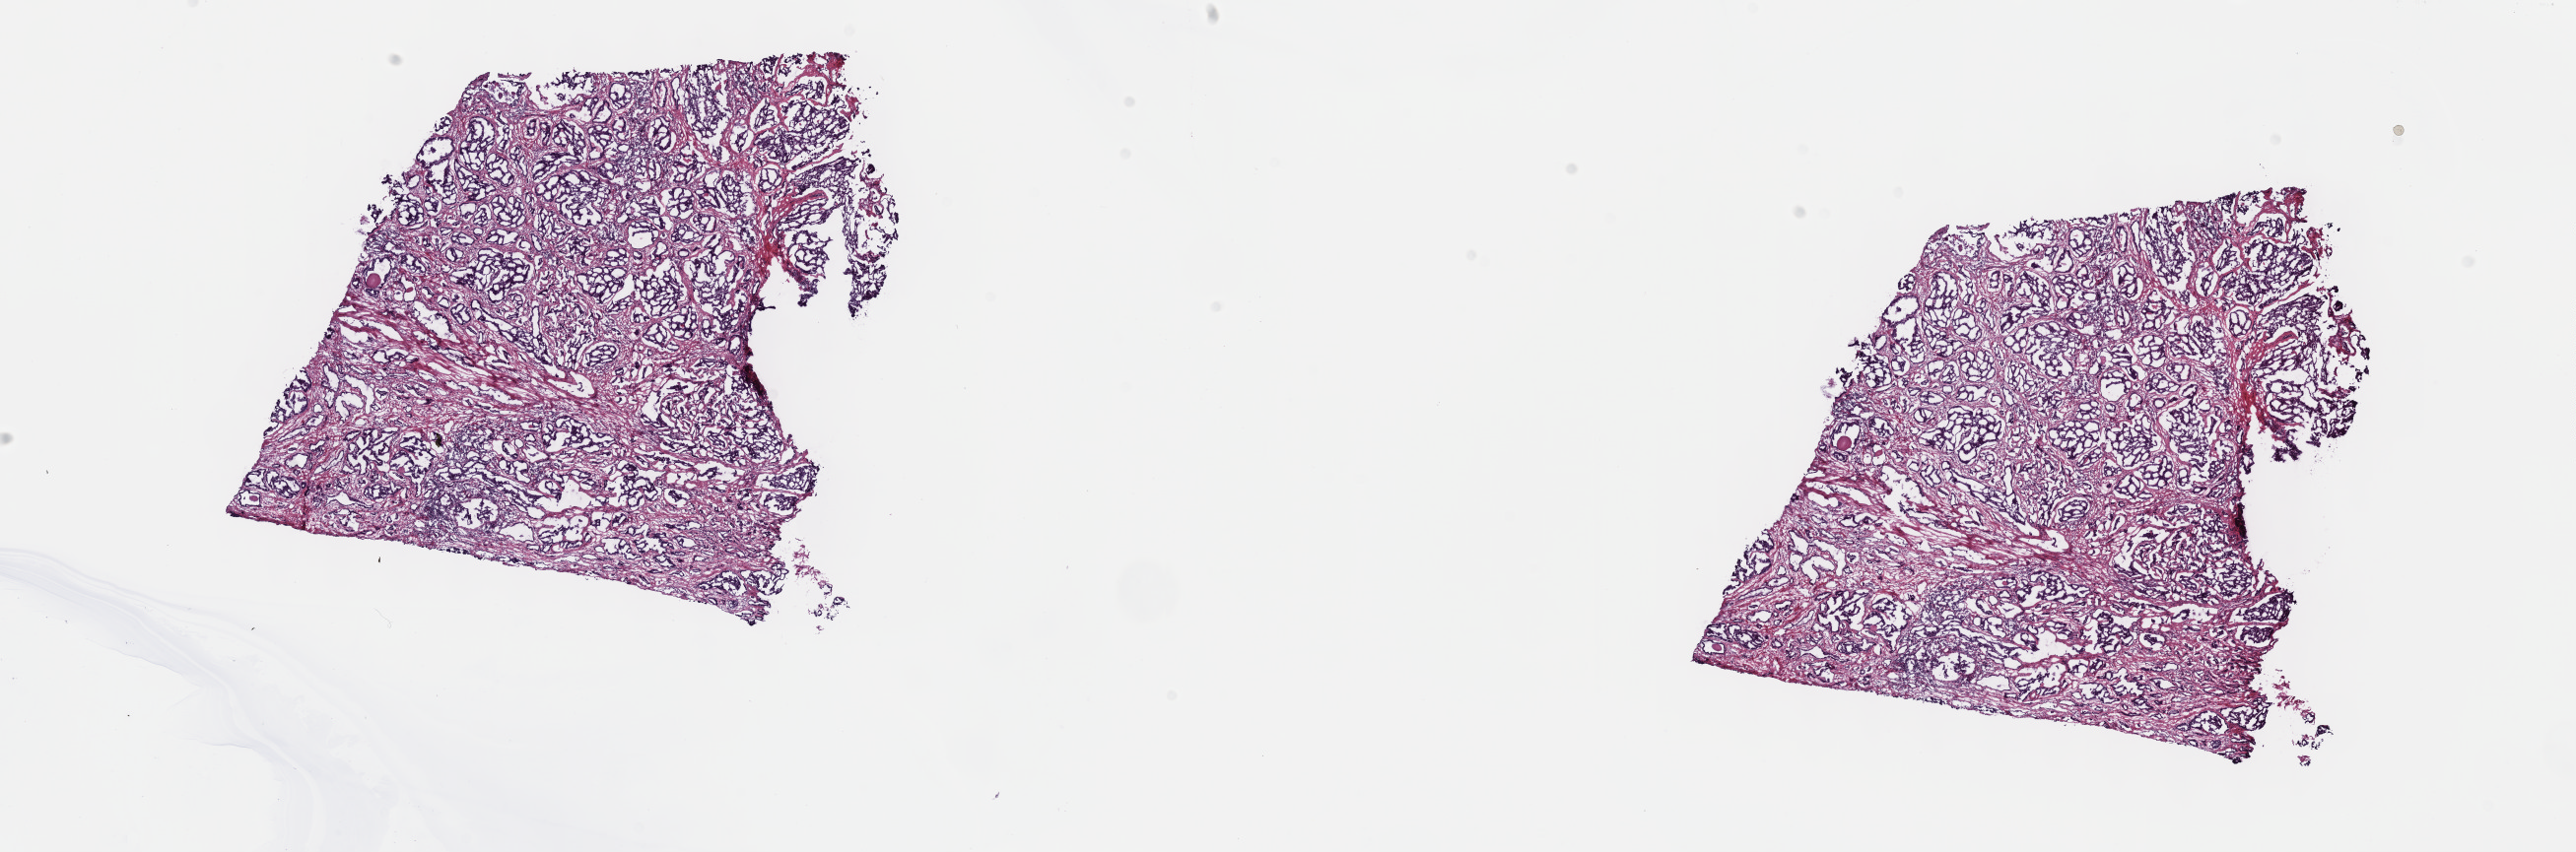
Digitized H&E-stained tissue section (whole slide) — whole scanned area (about 21.1 x 7.0 mm) shown as a low-resolution overview. Frozen section from the top of the tissue portion. Sample: primary tumour, prostate. Male, age 55 years at initial diagnosis. Slide review estimates, as recorded: tumour cells 62%, tumour nuclei 85%.
Histologic diagnosis: Adenocarcinoma, NOS (prostate gland).